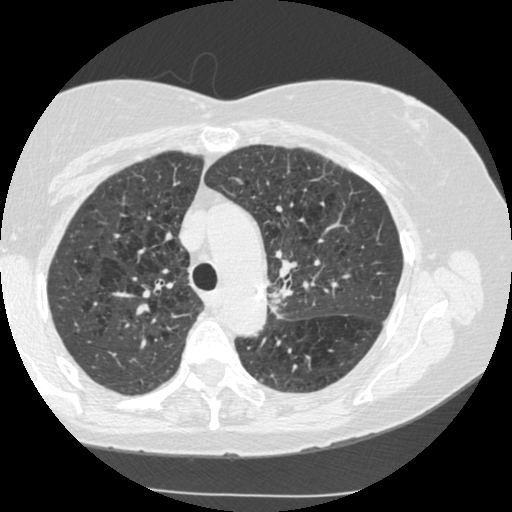
Chest CT (low-dose screening protocol), one axial image; second annual screen; lung window (W 1500 / L -600 HU); 1.25 mm slice thickness; standard (soft-tissue) reconstruction kernel (STANDARD); slice 186 of 249 in the series; 512 × 512 image matrix. Female, age 70 years at enrolment.
Expert-annotated lung lesion, bounding box <248,266,318,329> (left, top, right, bottom; pixels). The exam's reader record, not a measurement of the box and not confirmed to be the same lesion: non-calcified nodule or mass ≥4 mm, left upper lobe, 15 × 13 mm, spiculated (stellate) margins, soft tissue attenuation, pre-existing on the prior screen: yes; interval growth: yes. Official screen result: positive, other.